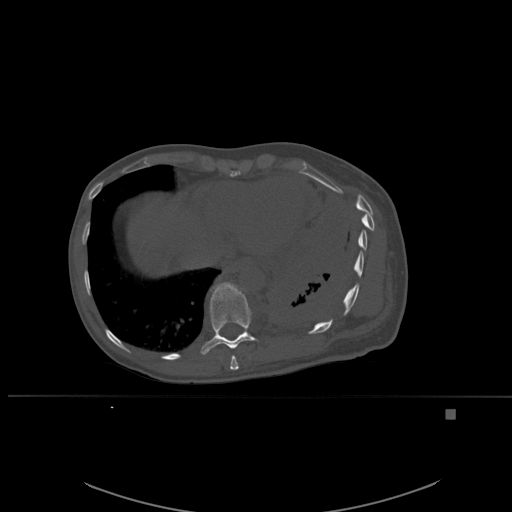
CT including the spine, one axial slice; position 318 of 537 along the scan axis; bone window (W 1800 / L 400 HU); 1.5 mm slice thickness; 512 × 512 image matrix, field of view 440 × 440 mm. Patient: female, 45 years. Case-level facts recorded for this patient, not image findings: primary cancer: lung.
Annotated regions visible in this slice (semi-automatic segmentation, software-assisted and operator-edited):
- T10 vertebra: bounding box <200,282,258,355> (left, top, right, bottom; pixels)
- T9 vertebra: <230,355,239,370>